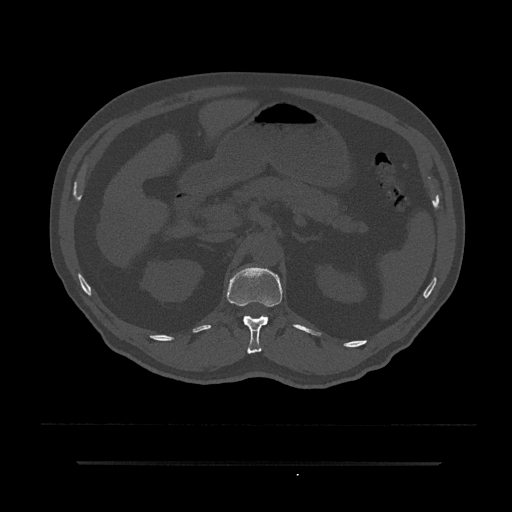
CT including the spine, one axial slice; slice 192 of 797 in the series (ordered by position); 120 kVp; bone window (W 1800 / L 400 HU); 0.5 mm slice thickness; 512 × 512 image matrix, field of view 464 × 464 mm. Patient: male, 59 years. Case-level facts recorded for this patient, not image findings: primary cancer: bile ducts; vertebrae with lytic lesions (as recorded): T10.
Outlined on this slice (semi-automatic segmentation, software-assisted and operator-edited):
- T12 vertebra: bounding box (x1, y1, x2, y2) in pixels: (227, 266, 282, 354)